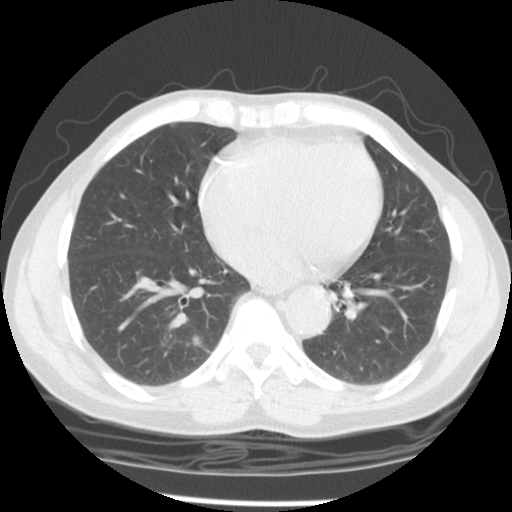
Axial slice from a low-dose chest CT screening exam. Third screening round (two years after baseline). Lung window (W 1500 / L -600 HU). 2.5 mm slice thickness. Standard (soft-tissue) reconstruction kernel (STANDARD). Slice 54 of 127 in the series. Male, age 58 years at enrolment. Current smoker at enrolment.
Expert reader's lesion annotation, bounding box [x1, y1, x2, y2] px = [169, 325, 214, 362]. The screening reader recorded 2 non-calcified nodules or masses ≥4 mm on this exam (left upper lobe, right lower lobe); which of them this box marks is not recorded. Official screen result: positive, other. Later outcome: lung cancer diagnosed 323 days after this screen — adenocarcinoma, NOS, right lower lobe, poorly differentiated (G3), stage IIIA (AJCC 6th edition), 15 mm at pathology.